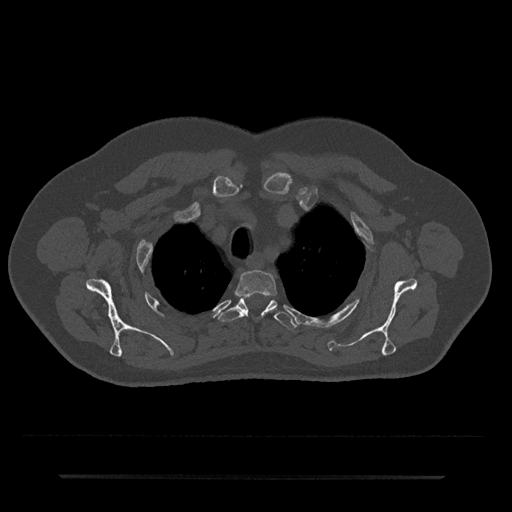
CT including the spine, one axial slice; position 583 of 797 along the scan axis; 120 kVp; bone window (W 1800 / L 400 HU); 512 × 512 image matrix, field of view 437 × 437 mm. Patient: male, 69 years. Case-level facts recorded for this patient, not image findings: primary cancer: prostate.
Annotated regions visible in this slice (semi-automatically segmented with operator editing):
- T2 vertebra: bounding box <235,270,277,298> (left, top, right, bottom; pixels)
- T3 vertebra: <219,298,298,330>